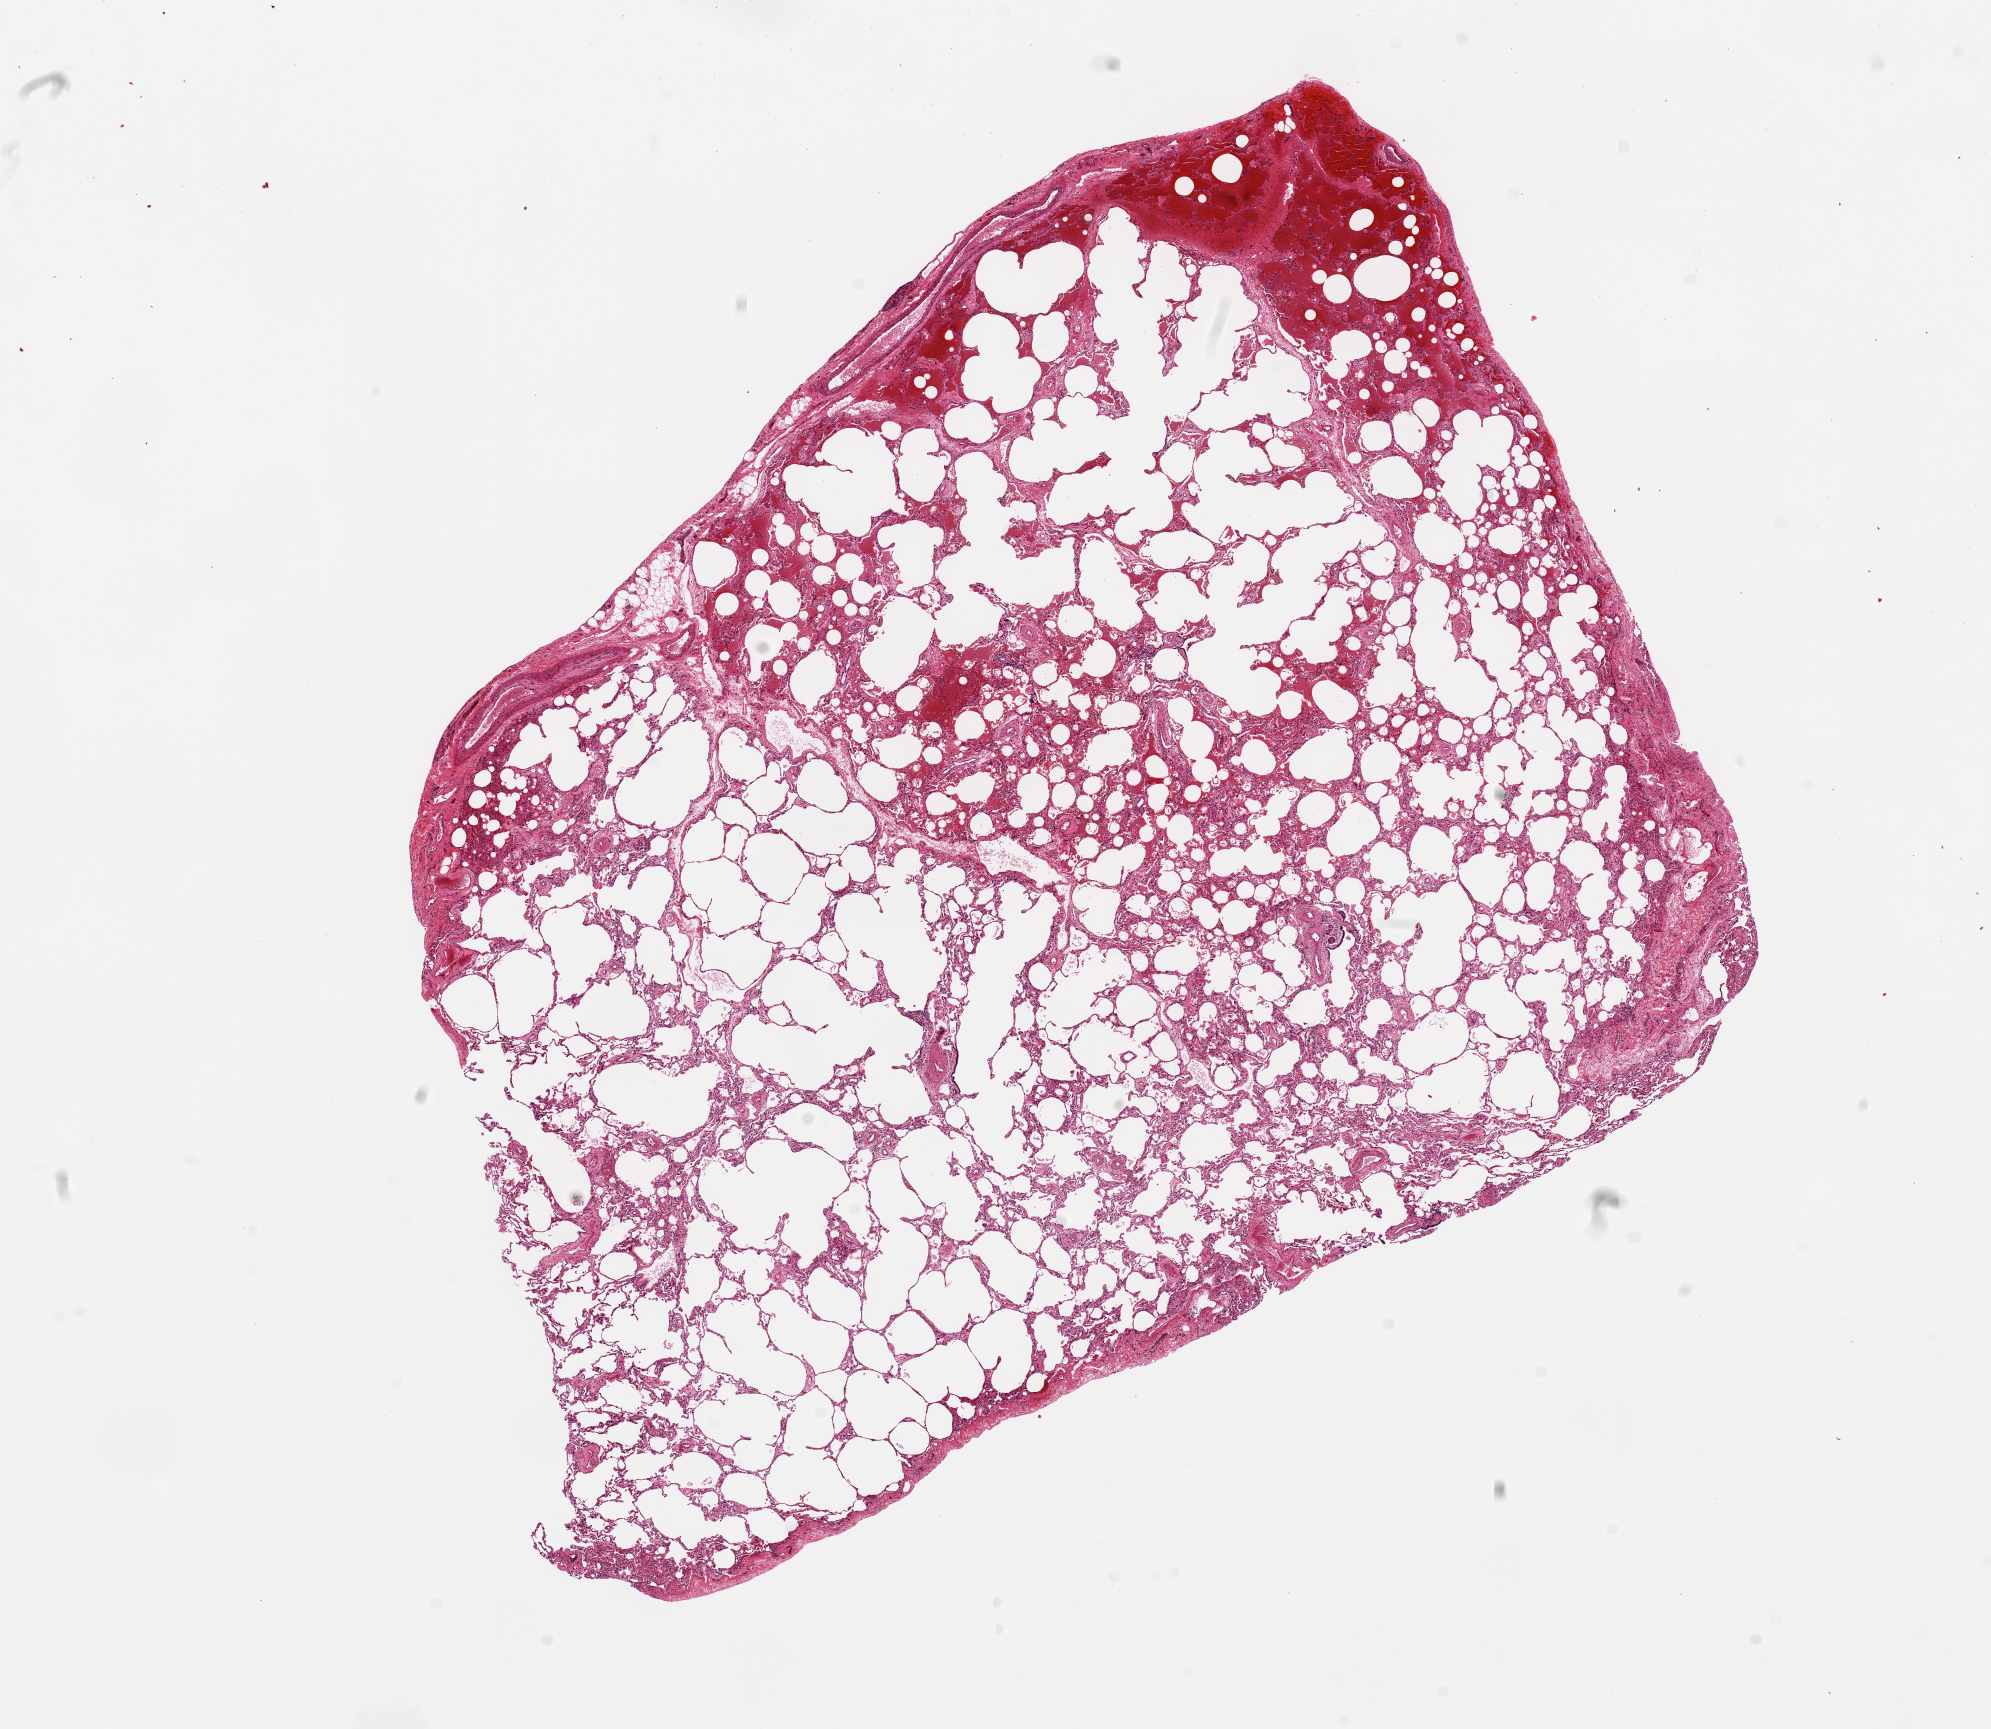
Digitized haematoxylin and eosin-stained section, low-resolution overview of the scanned area, about 15.8 x 13.7 mm; PAXgene-fixed paraffin-embedded (PFPE) section; sampled site (target tissue): lung; tissue donor sample. Donor: male.
- review note (as recorded): Moderate emphysema, vascular sclerosis. Focal hemorrhage. 10x8.6mm